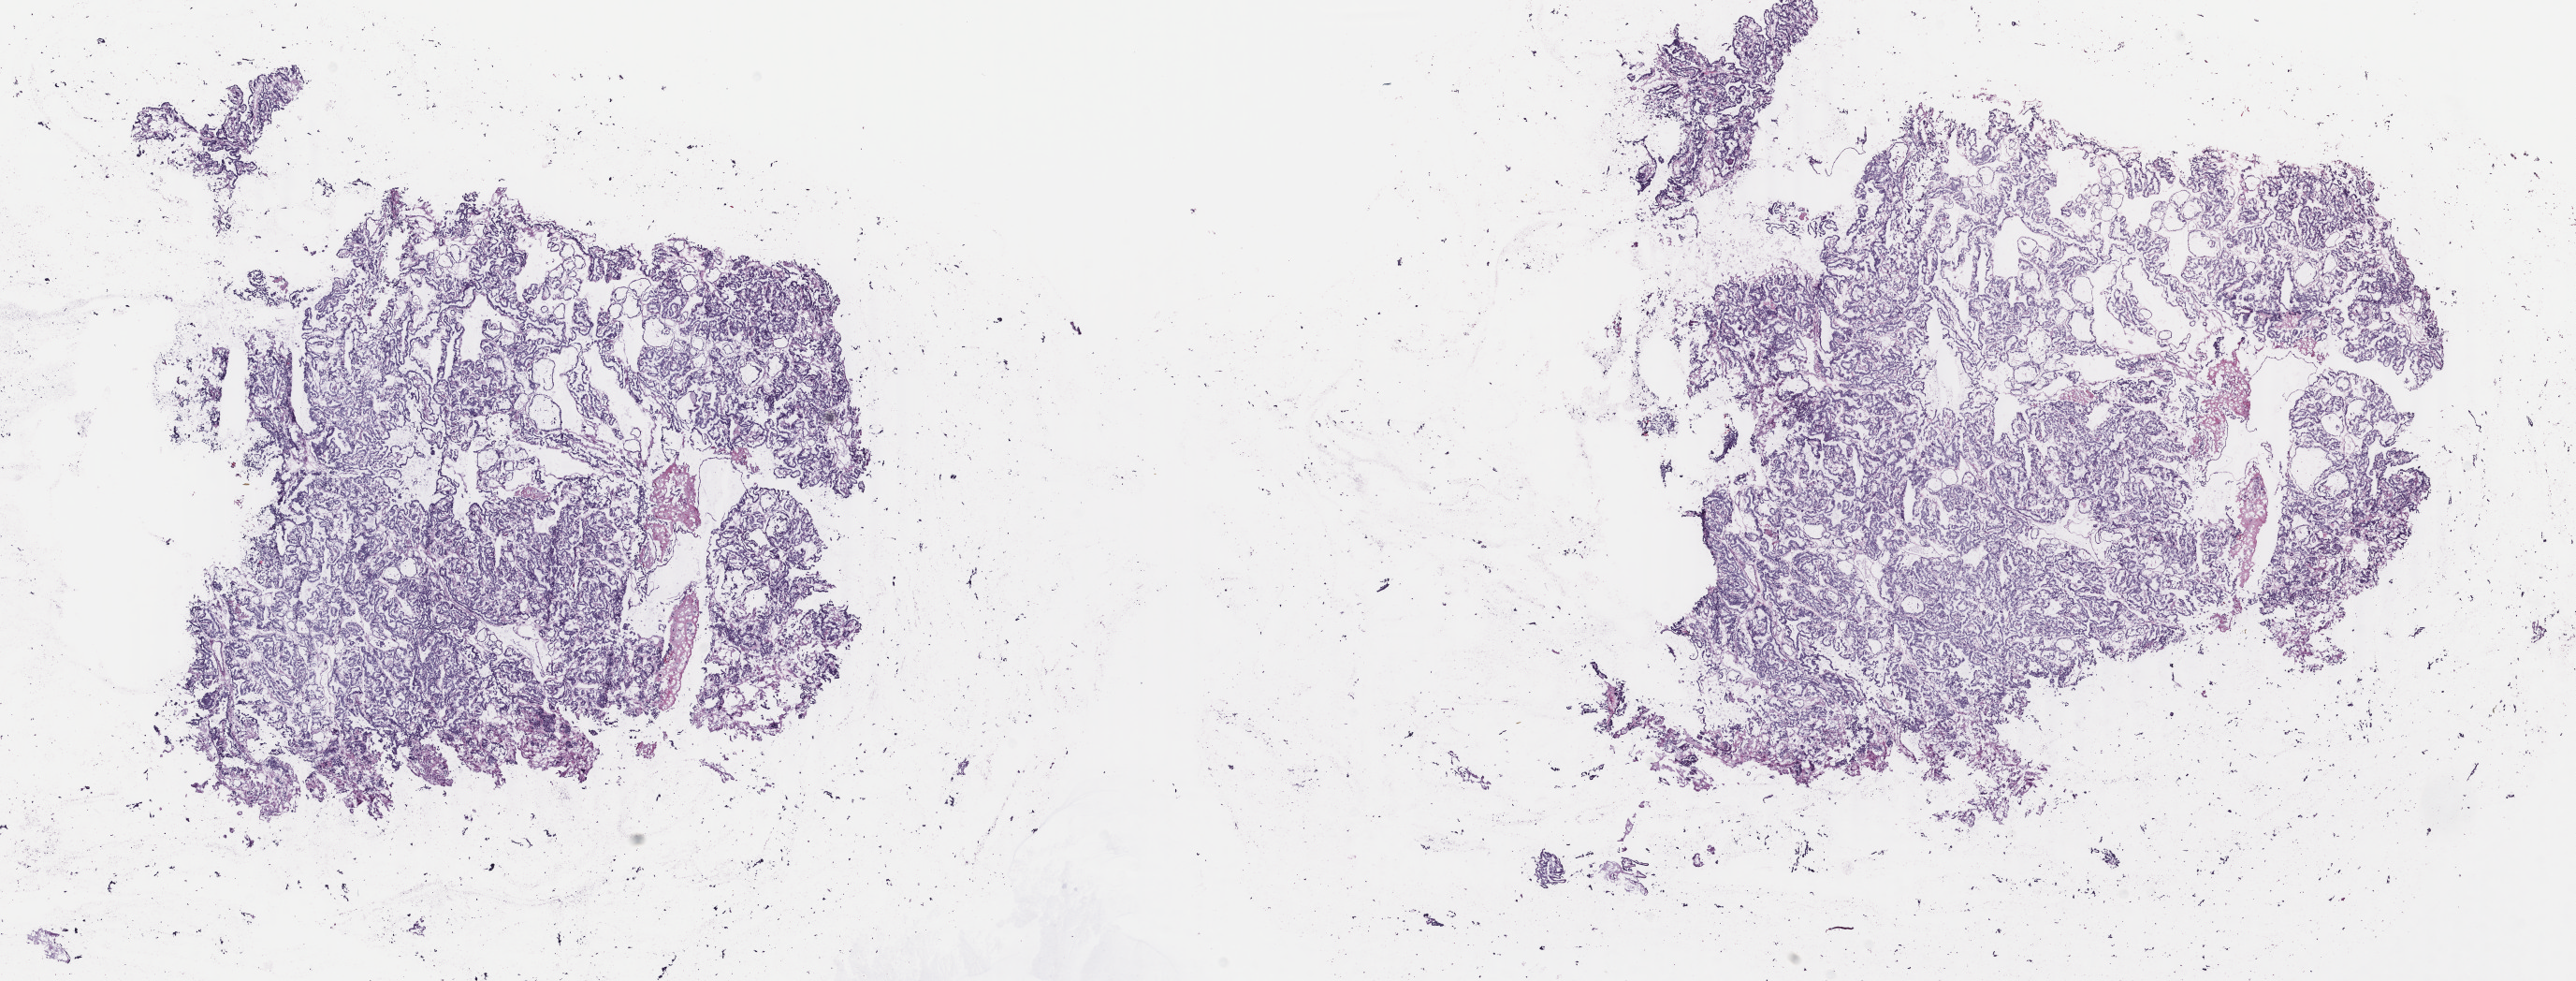
H&E-stained whole-slide image — shown as a low-resolution overview of the whole scanned area (about 21.9 x 8.3 mm, from a 40x scan). Frozen section from the top of the tissue portion. Sample: primary tumour, thyroid. Female, age 37 years at initial diagnosis. Slide review estimates, as recorded: tumour cells 100%, tumour nuclei 95%, normal cells 0%, stromal cells 0%, necrosis 0%. Inflammatory infiltration, as recorded: lymphocyte infiltration 0%, monocyte infiltration 0%, neutrophil infiltration 0%.
• laterality: right
• histologic diagnosis: Papillary adenocarcinoma, NOS (thyroid gland)
• lymph nodes positive (case pathology): 0 of 7 examined
• AJCC pathologic stage: I